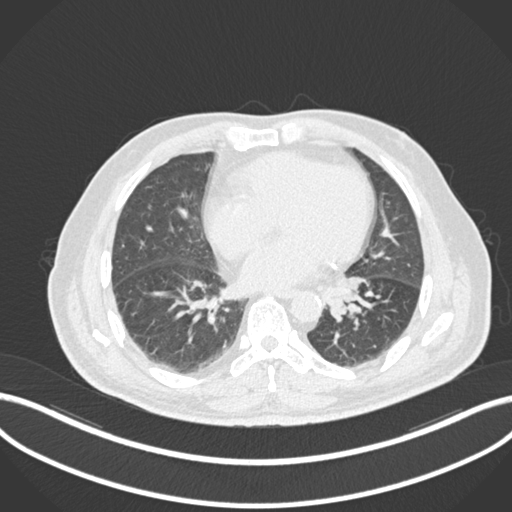
Chest CT, one axial slice; slice 44 of 161 in the series (ordered by position); lung window (W 1500 / L -600 HU); 512 × 512 image matrix. Male patient, age 71 years. Case-level facts recorded for this patient, not image findings: clinical TNM (as recorded): T1b N0 M0.
Annotated regions visible in this slice (rectangle marked by the reading radiologist):
- lung tumour (recorded histology: squamous cell carcinoma): box from (x=326, y=275) to (x=371, y=323) px